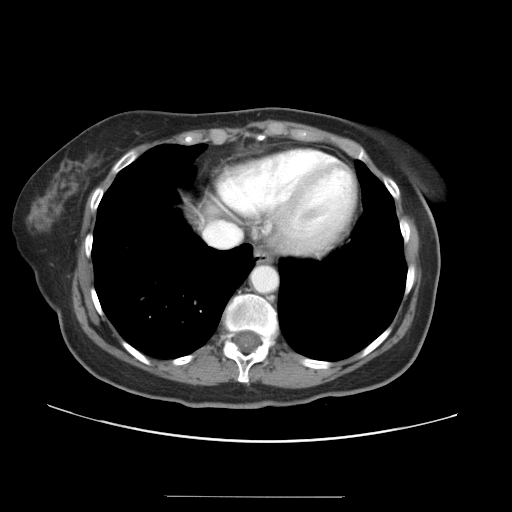
Contrast-enhanced abdominal CT, one axial slice; position 32 of 34 along the scan axis; intravenous contrast given; soft-tissue window (W 400 / L 40 HU); 5 mm slice thickness; 512 × 512 image matrix, field of view 382 × 382 mm. Female patient, age 69 years. Case-level facts recorded for this patient, not image findings: diagnosis: colorectal cancer liver metastases, imaged before liver resection; multiple liver metastases: yes; largest metastasis: 1.4 cm; disease in both lobes: yes.
Structures marked on this image (outlined manually by an expert reader):
- hepatic veins: bounding box (x1, y1, x2, y2) in pixels: (204, 152, 335, 247)